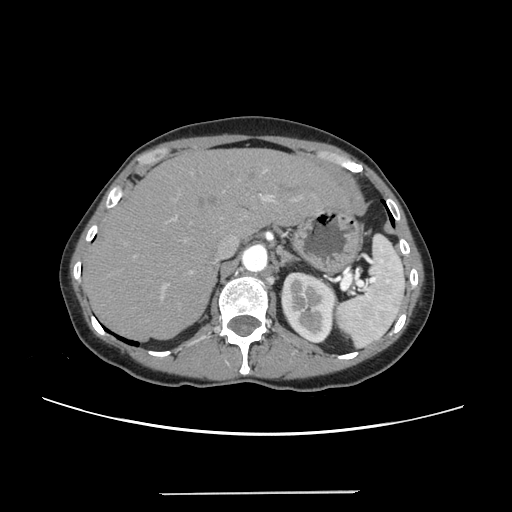
Contrast-enhanced abdominal CT, one axial slice; position 176 of 240 along the scan axis; 120 kVp; intravenous contrast given; soft-tissue window (W 400 / L 40 HU); 1.25 mm slice thickness; 512 × 512 image matrix, field of view 371 × 371 mm. Female patient, age 60 years. From the clinical record (not read from this slice): diagnosis: colorectal cancer liver metastases, imaged before liver resection; multiple liver metastases: no; largest metastasis: 1.5 cm.
Outlined on this slice (outlined manually by an expert reader):
- liver: bounding box (x1, y1, x2, y2) in pixels: (86, 150, 349, 340)
- planned liver remnant (the part of the liver to remain after resection): (86, 150, 349, 340)
- portal vein (with intrahepatic branches): (134, 170, 300, 297)